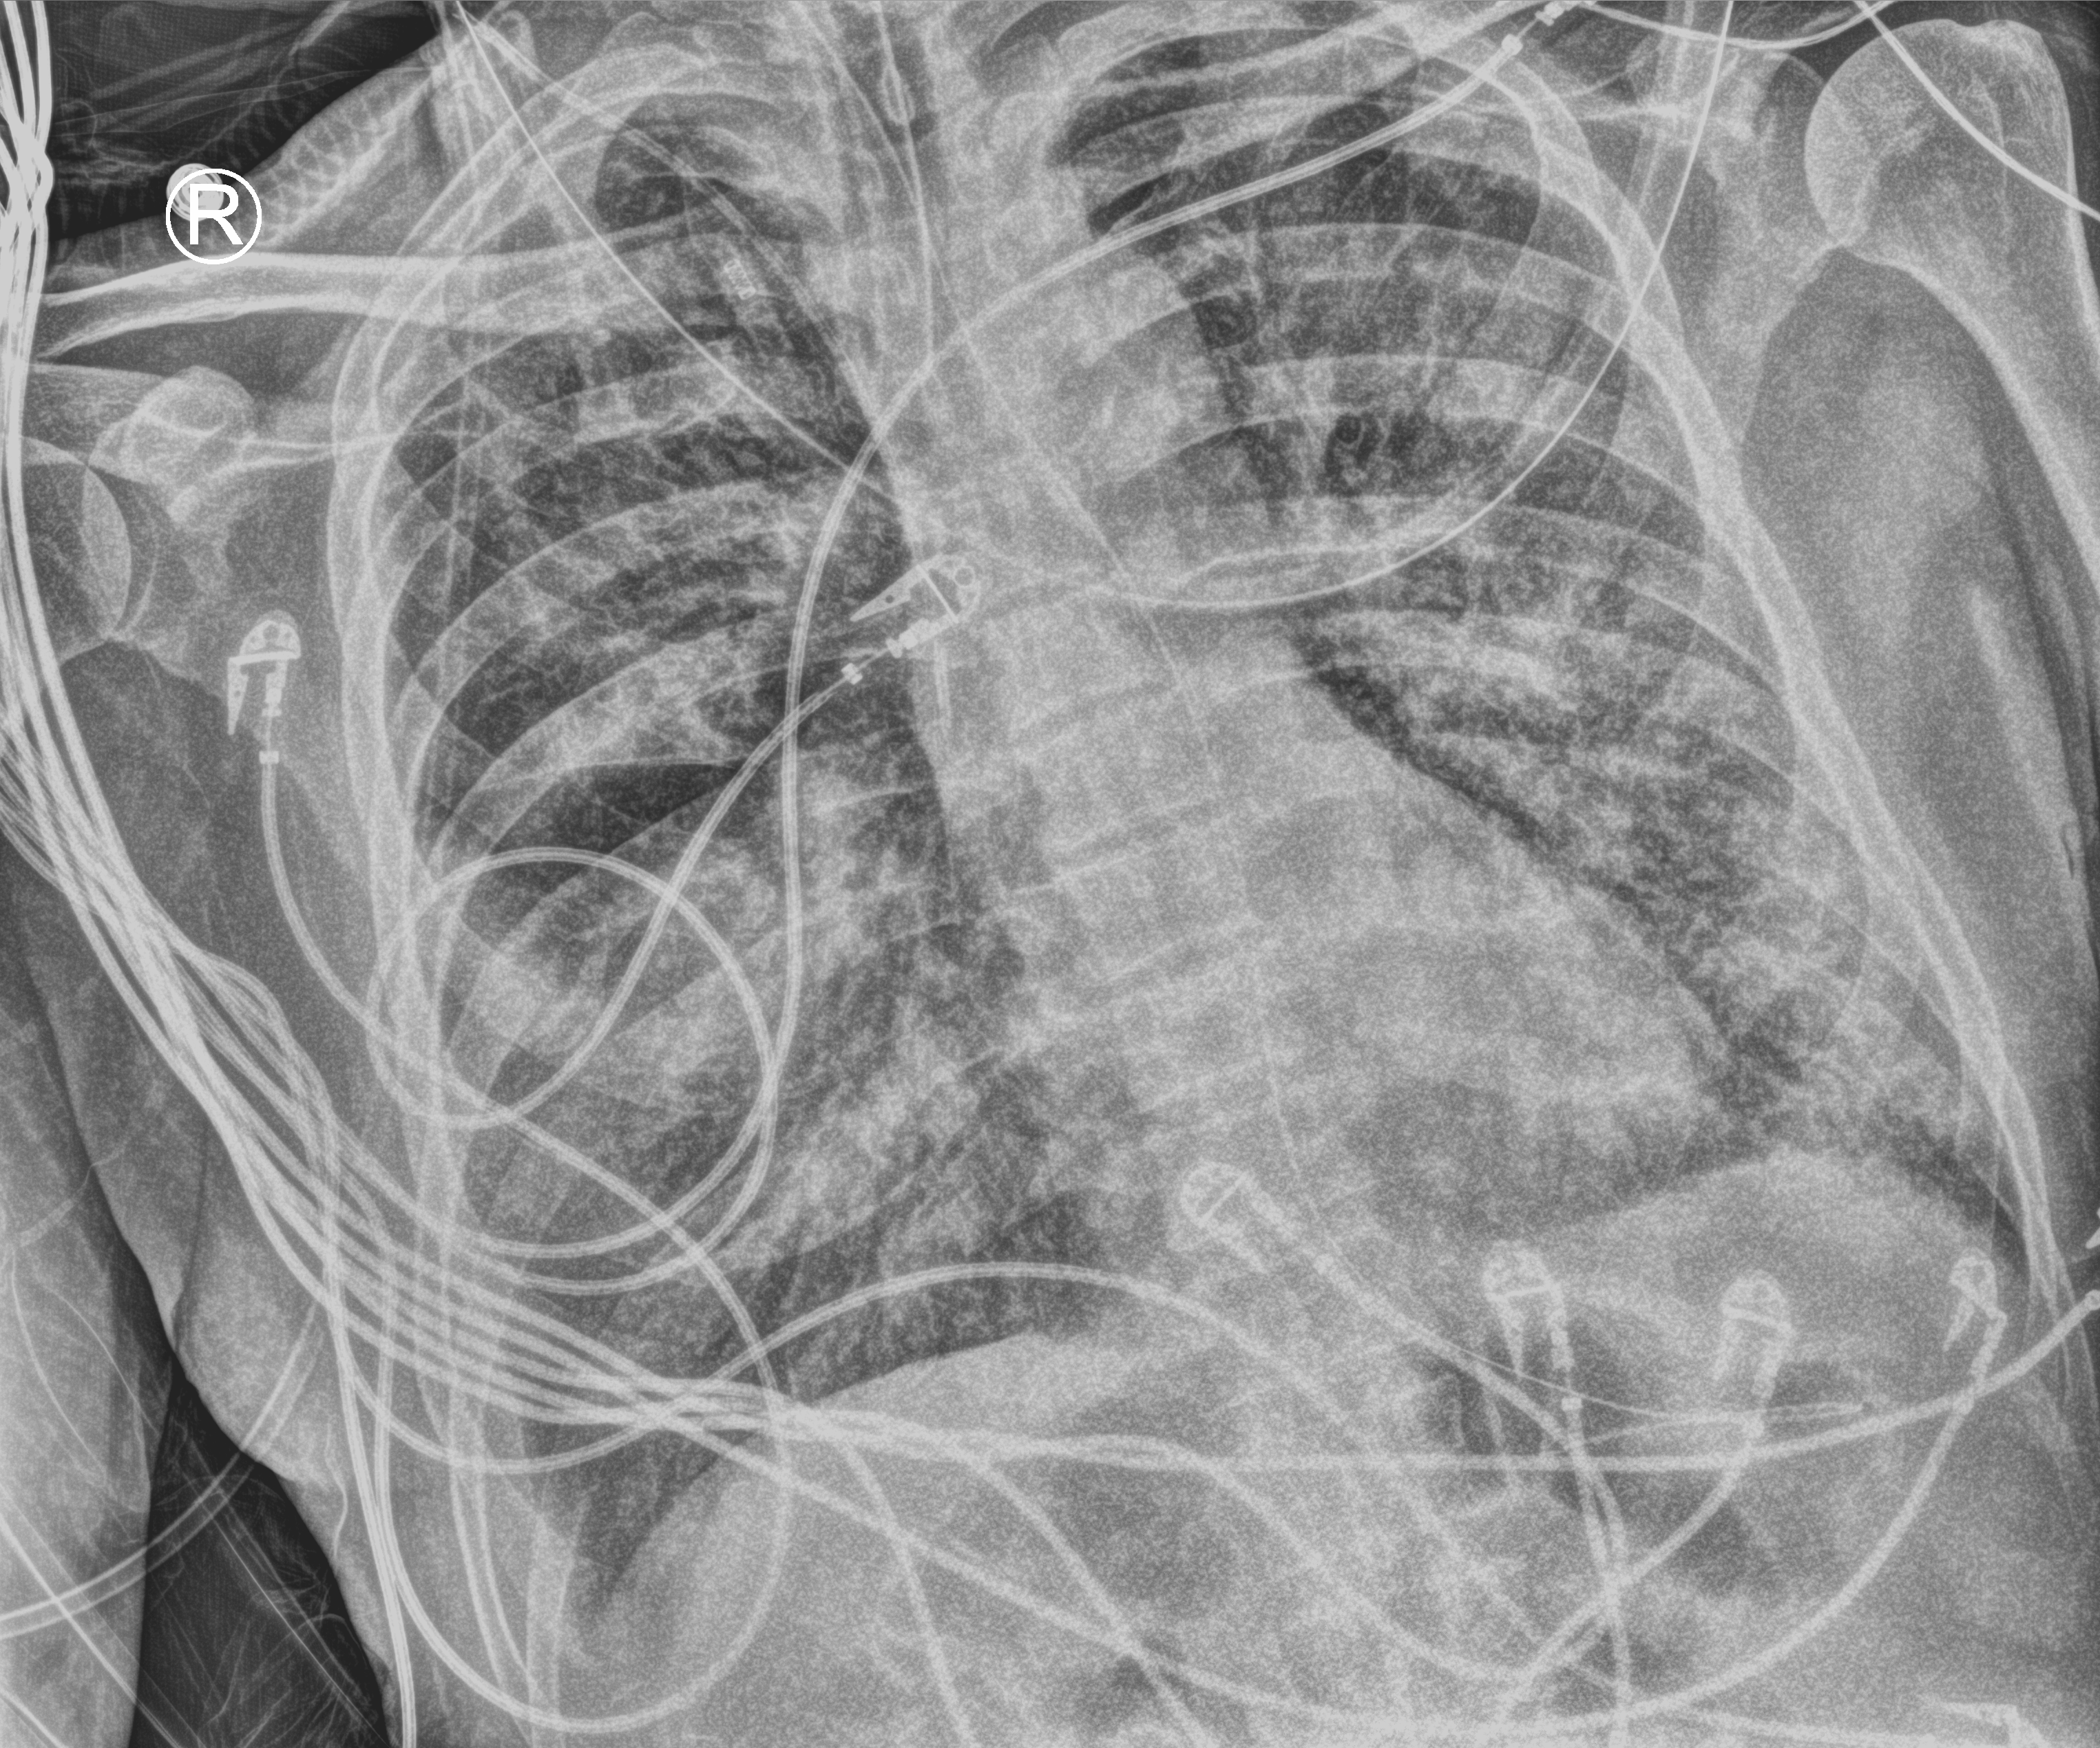
Bedside chest radiograph (computed radiography); anteroposterior (AP) projection. Male patient hospitalised with COVID-19, age 60–74 years.
Hospital-stay facts (about this admission, not read from this image; timing relative to this image not recorded): COPD (admission record): no; mechanically ventilated during this hospital stay: yes; admitted to intensive care during this hospital stay: yes.